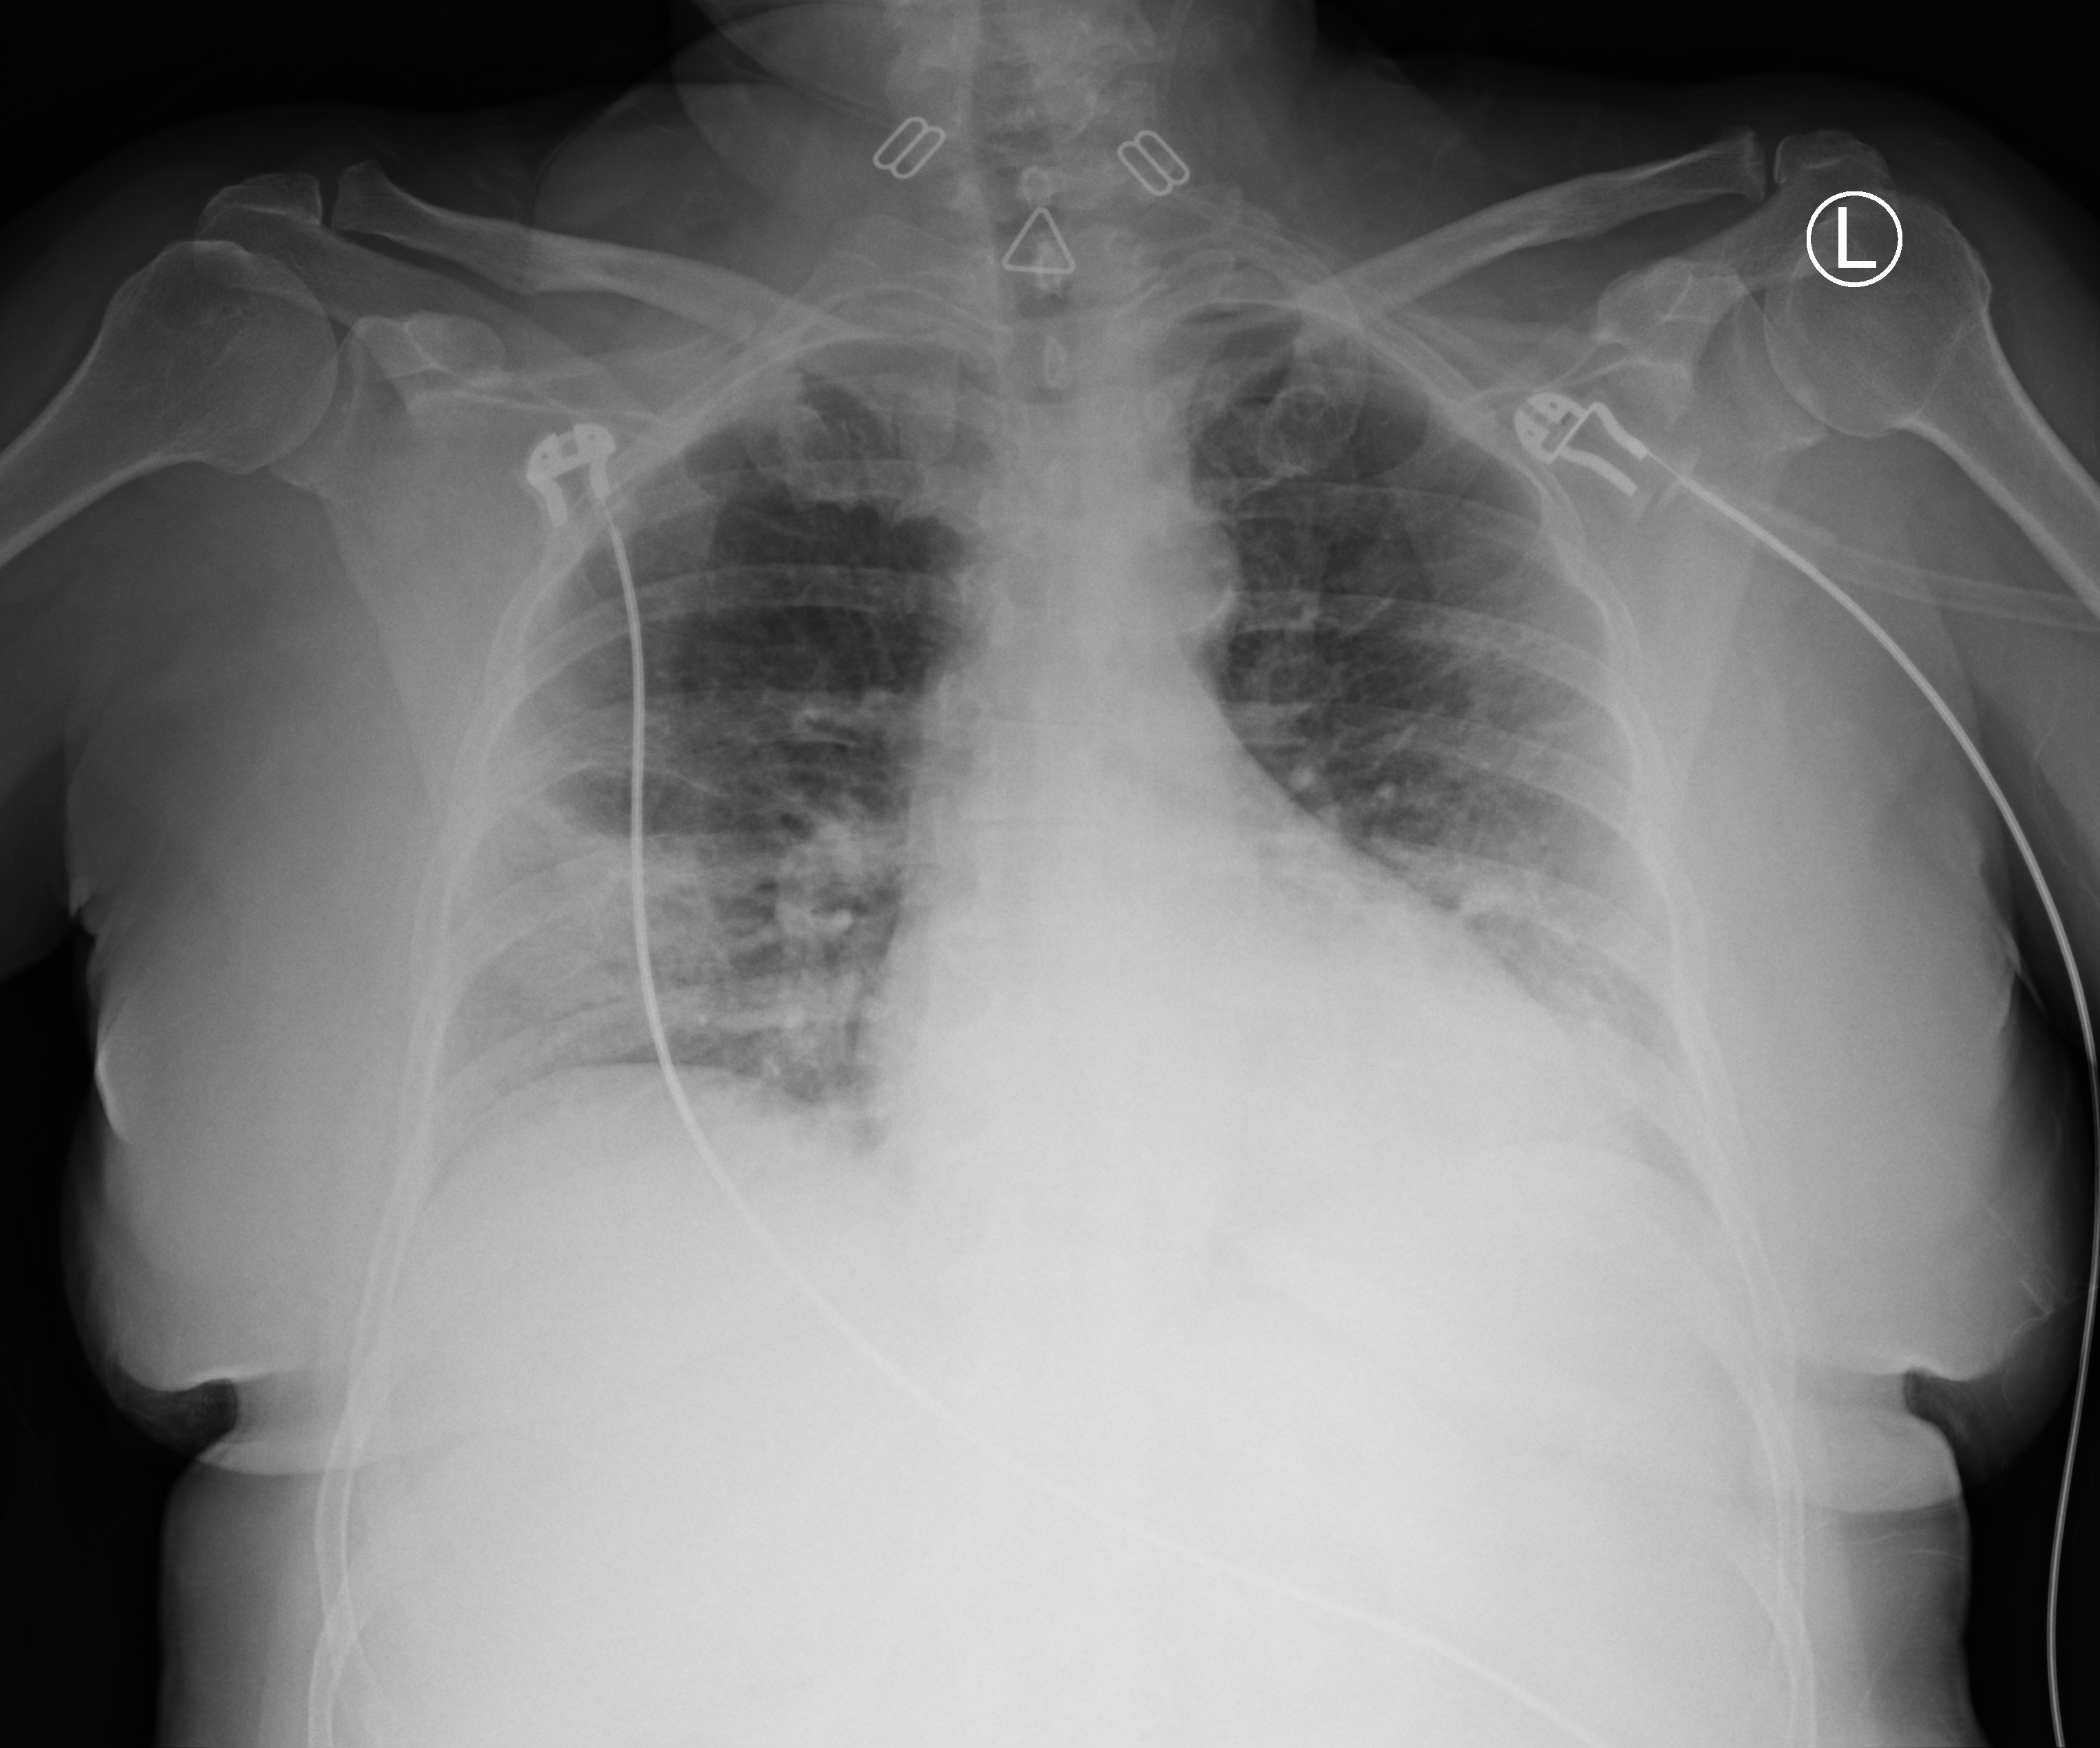
Bedside chest radiograph (computed radiography); anteroposterior (AP) projection. Patient hospitalised with COVID-19; female, aged 60–74 years.
From the hospital-stay record, not from the radiograph (when in the stay this image was taken is not recorded):
- mechanically ventilated during this hospital stay: yes